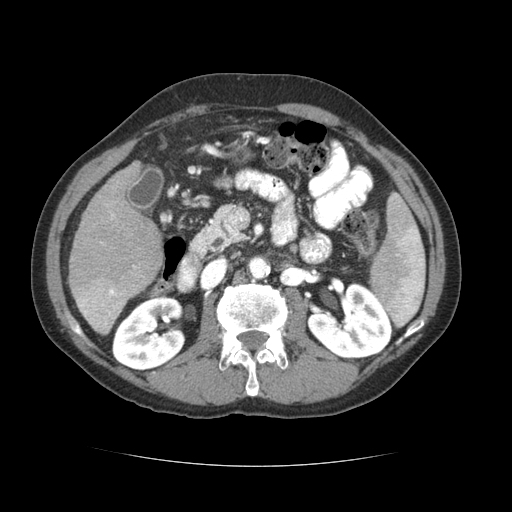
Contrast-enhanced abdominal CT (liver protocol), one axial slice; position 27 of 69 along the scan axis; reconstruction kernel STANDARD; soft-tissue window (W 400 / L 40 HU); 2.5 mm slice thickness; 512 × 512 image matrix, field of view 360 × 360 mm. Case-level facts recorded for this patient, not image findings: diagnosis: hepatocellular carcinoma (patient treated with transarterial chemoembolisation; whether this scan precedes or follows treatment is not stated here); TNM stage (as recorded): Stage-II; Child-Pugh class: B; tumour differentiation: poorly differentiated; tumour size: 2.6 cm.
Outlined on this slice (semi-automatically segmented with operator editing):
- liver parenchyma outside the tumour (the mass and vessels are separate outlines, so this box may not span the whole liver): bounding box <68,162,162,334> (left, top, right, bottom; pixels)
- liver vessels: <77,213,137,327>